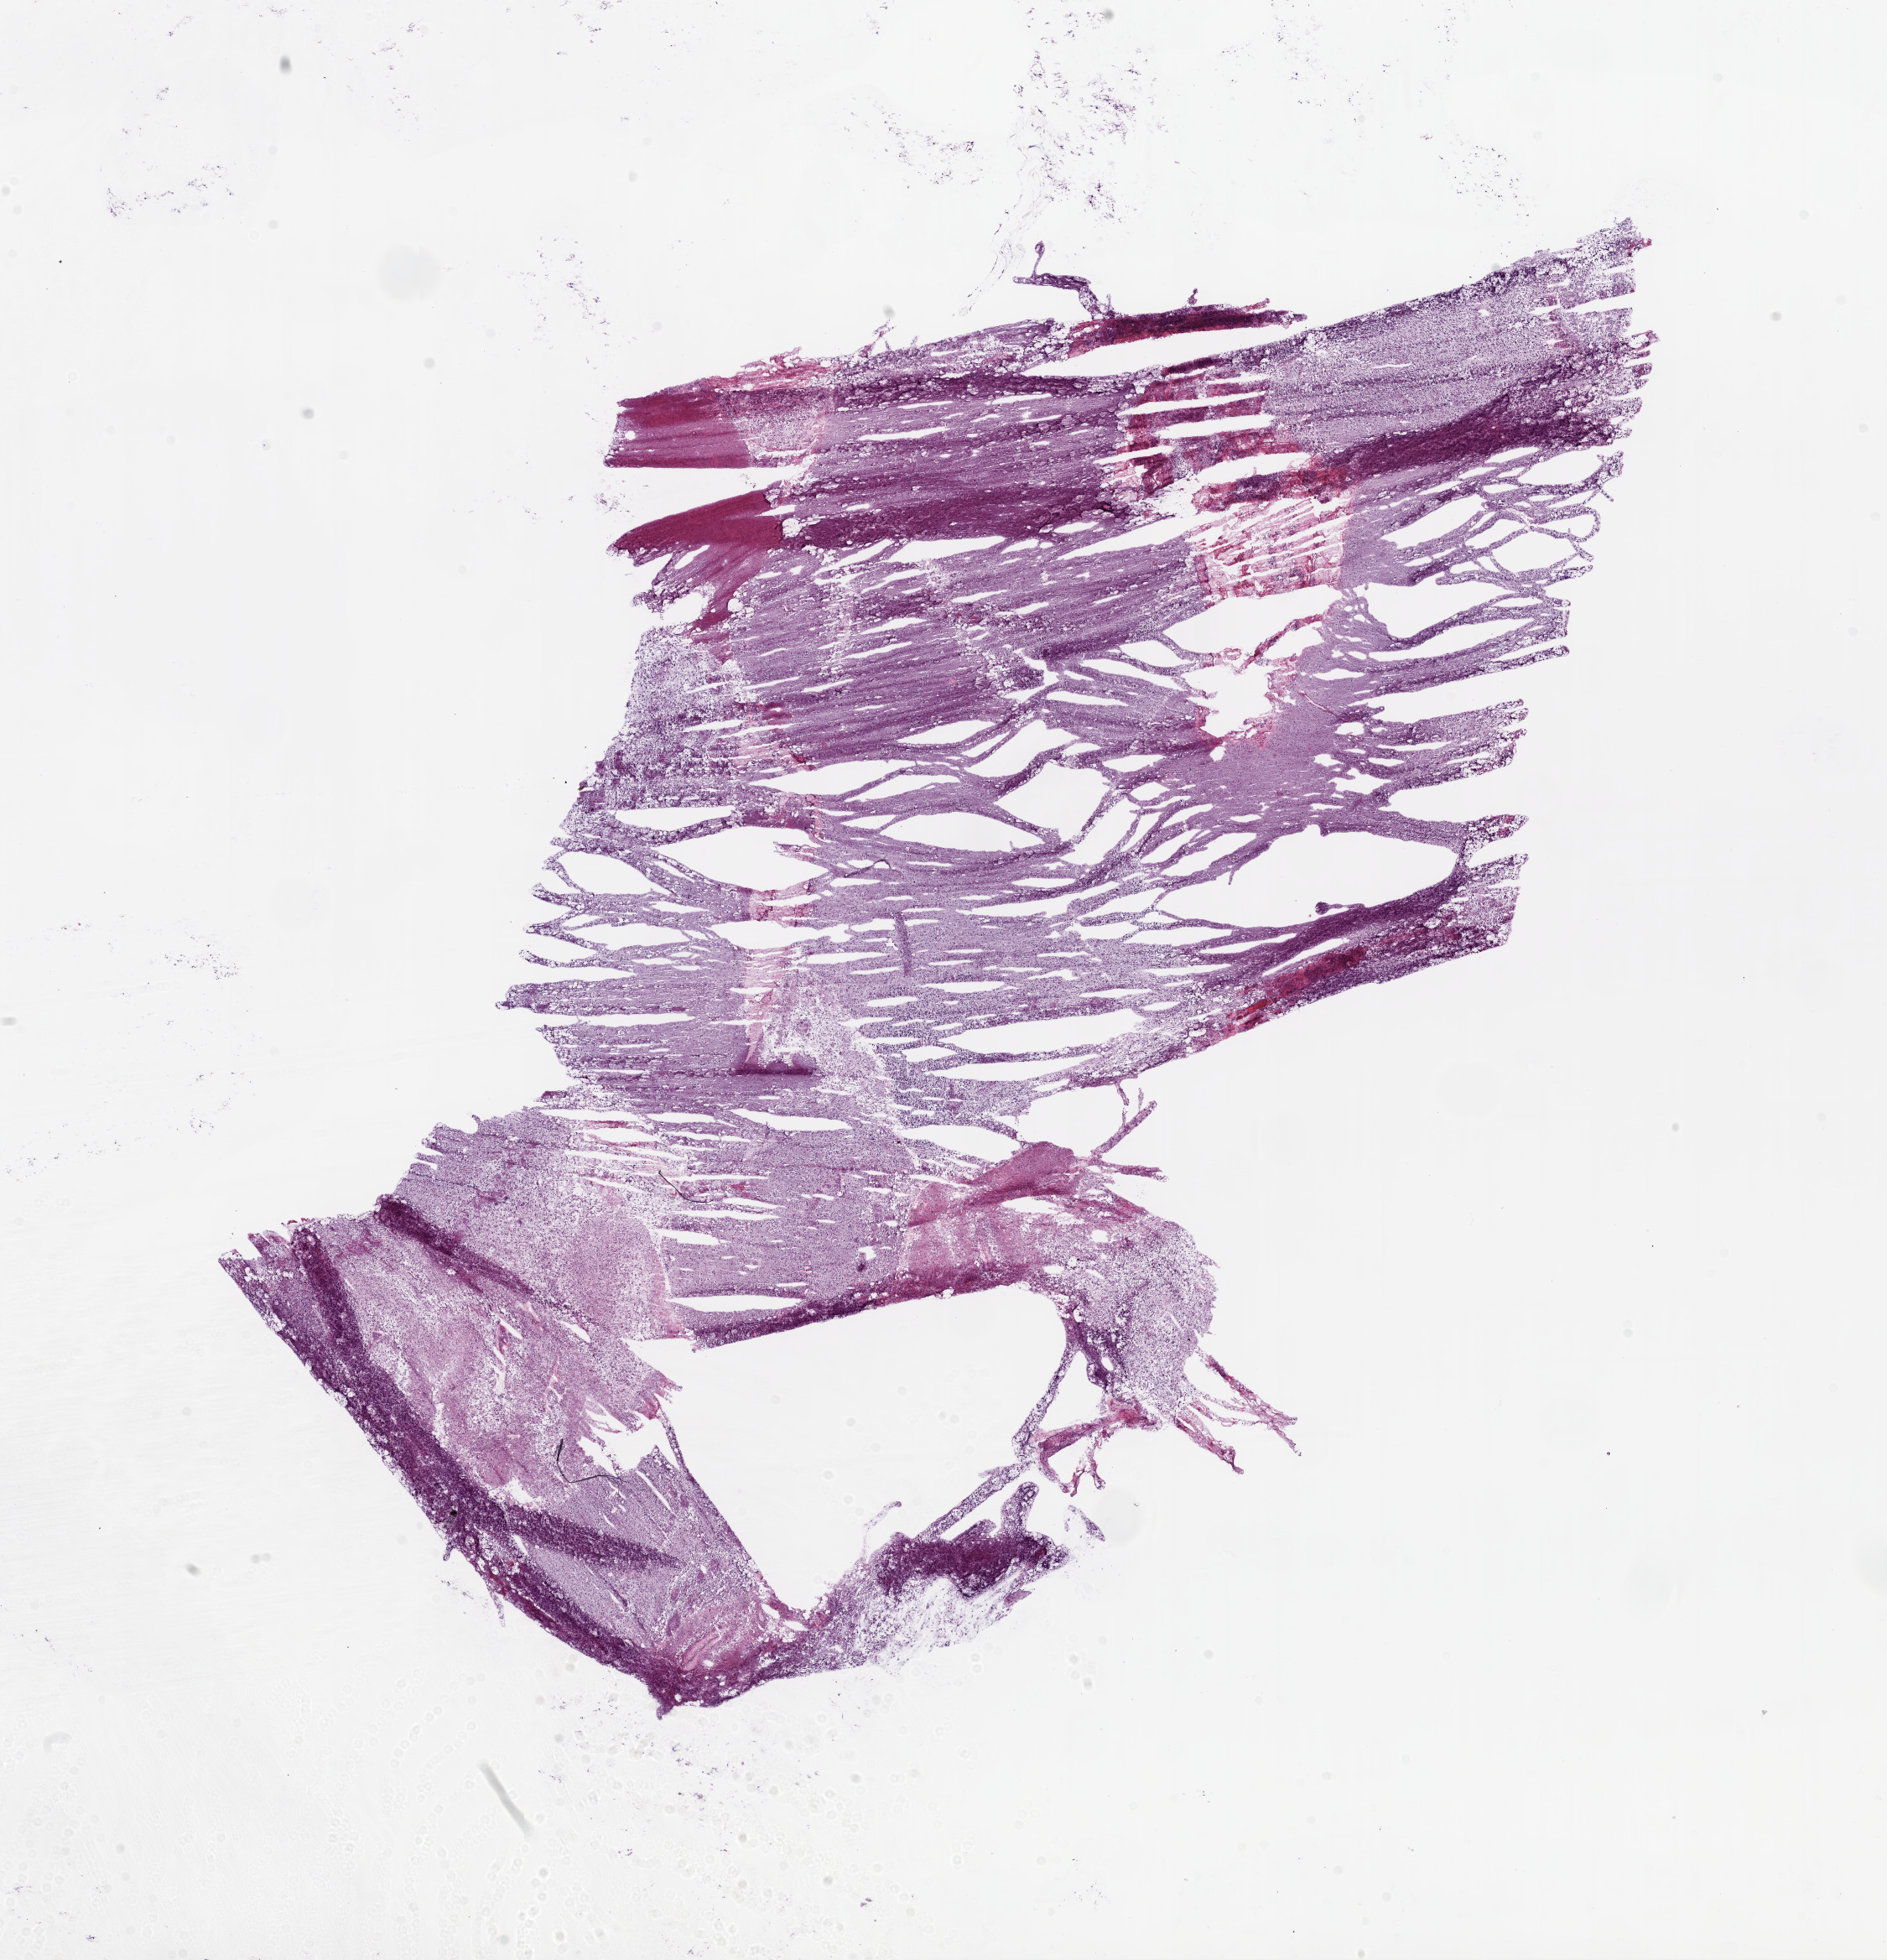
Whole-slide histology image, Hematoxylin and eosin (H&E) stained, whole scanned area (about 18.1 x 18.8 mm, slide scanned at 20x) shown as a low-resolution overview, frozen section from the bottom of the tissue portion, sample: primary tumour, brain. Female patient; age at initial diagnosis 75 years. Slide review estimates, as recorded: tumour cells 95%, tumour nuclei 80%, normal cells 0%, stromal cells 0%, necrosis 5%.
* diagnosis: Glioblastoma